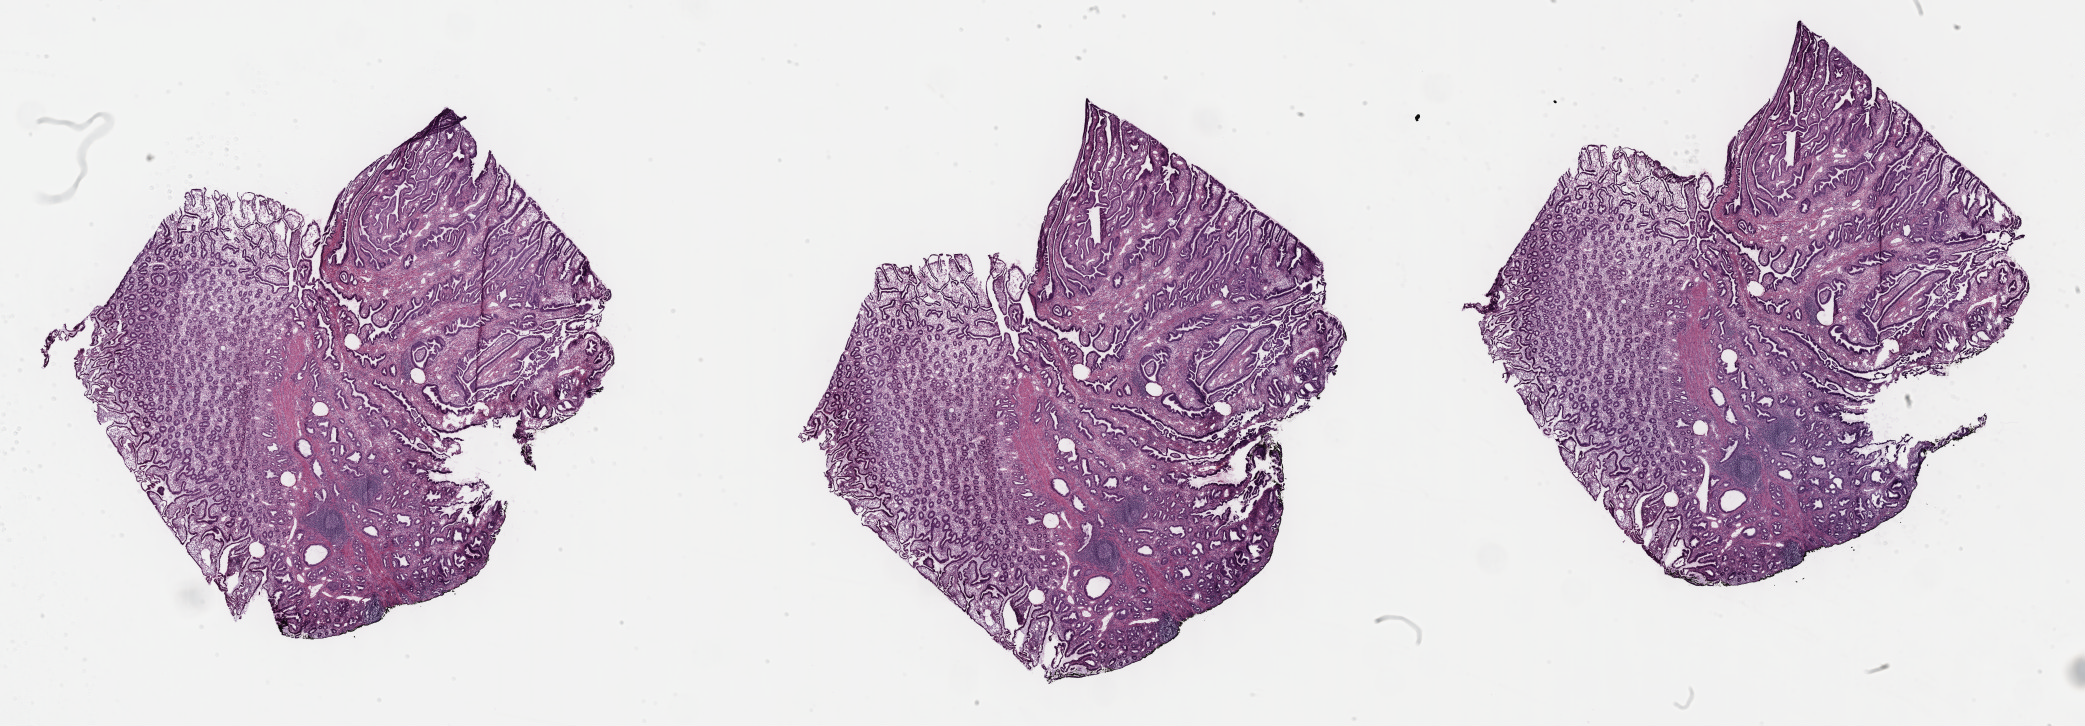
H&E-stained whole-slide image, shown as a low-resolution overview of the whole scanned area (about 33.7 x 11.7 mm, from a 40x scan); frozen section; sample: primary tumour, pancreas. Patient: female, age at initial diagnosis 60 years. Histologic grade: G2 (moderately differentiated). Composition of this section per pathologist review: tumour nuclei 20%, necrosis 0%.
Histologic diagnosis: Infiltrating duct carcinoma, NOS. AJCC pathologic stage: IIA. Lymph nodes positive (case pathology): 0 of 17 examined.